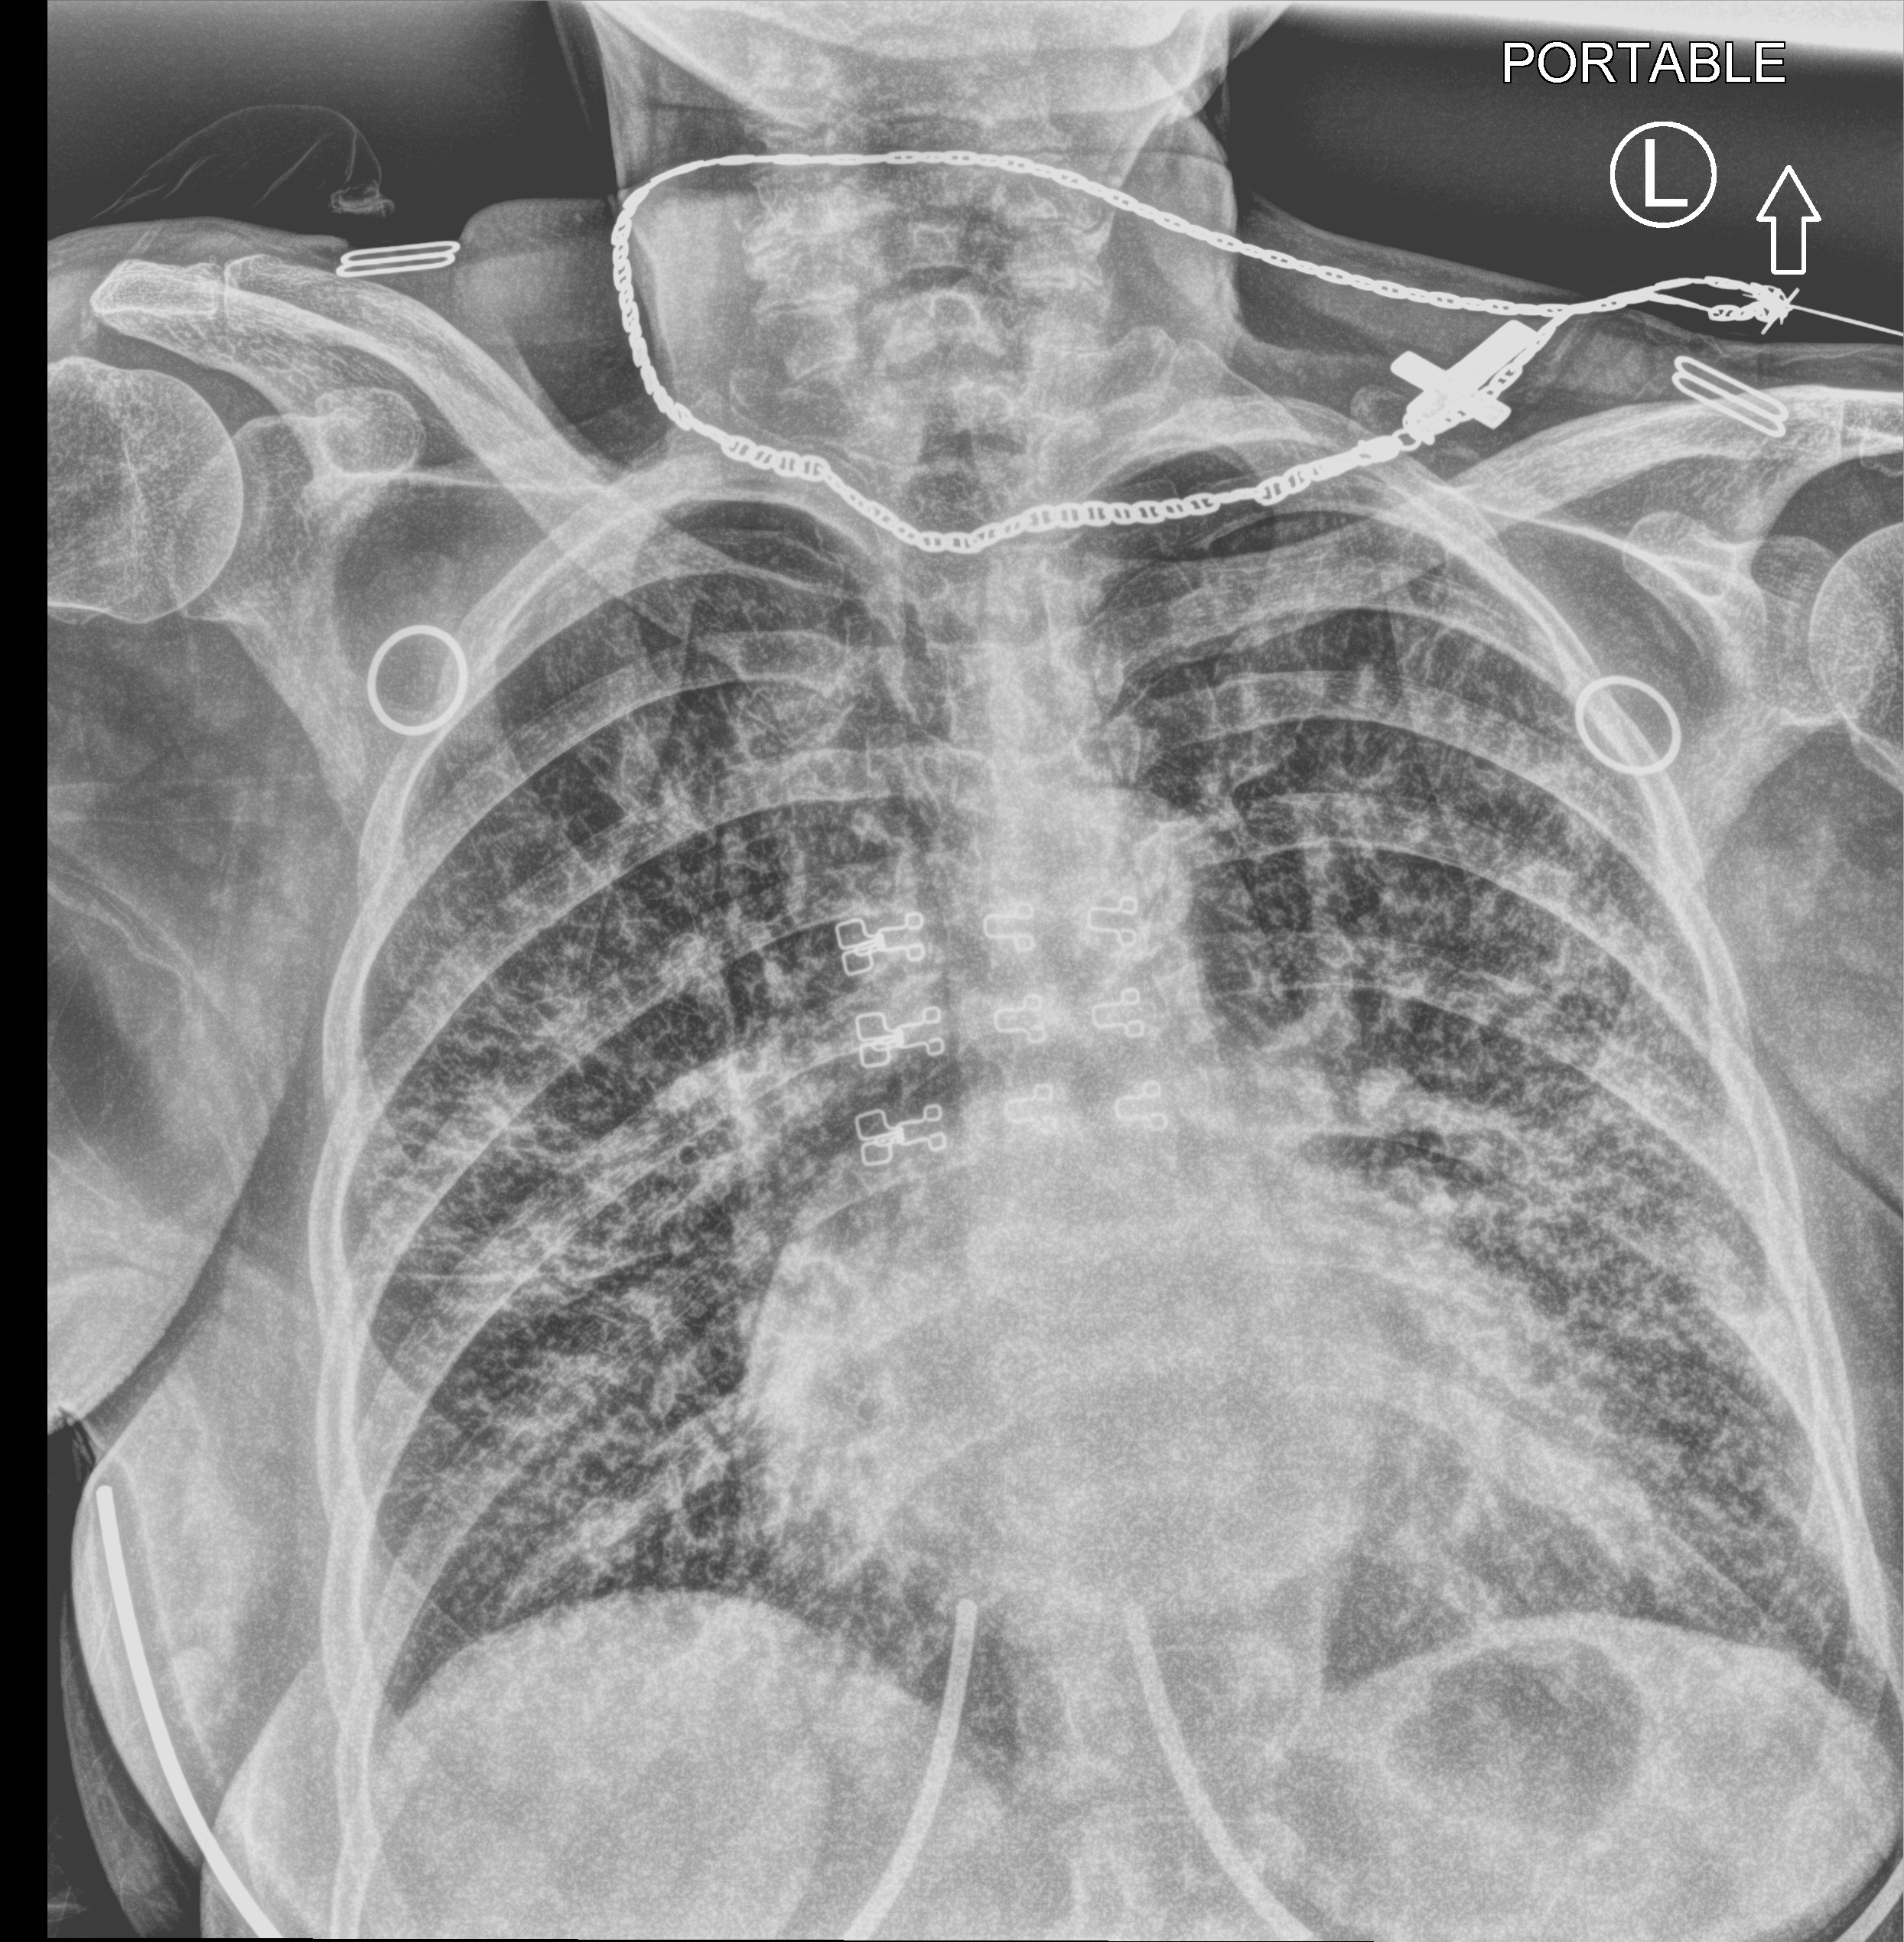
Chest X-ray (portable); anteroposterior (AP) projection. Female patient hospitalised with COVID-19, age 75–90 years.
From the hospital-stay record, not from the radiograph (when in the stay this image was taken is not recorded): mechanically ventilated during this hospital stay: no; other chronic lung disease (admission record): no.